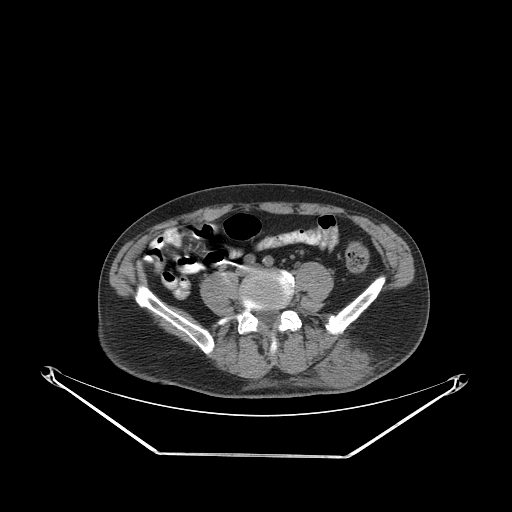
CT of an extremity soft-tissue mass (from a PET/CT study), one axial slice; slice 91 of 267 in the series (ordered by position); 140 kVp; soft-tissue window (W 400 / L 40 HU); 3.75 mm slice thickness; 512 × 512 image matrix, field of view 500 × 500 mm. Male patient. From the clinical record (not read from this slice): histological type: leiomyosarcoma; grade: intermediate; site of the primary tumour: left pelvis.
Annotated regions visible in this slice (expert contour drawn on MRI and transferred to this co-registered scan by the dataset authors):
- gross tumour volume (mass): bounding box <320,340,373,387> (left, top, right, bottom; pixels)